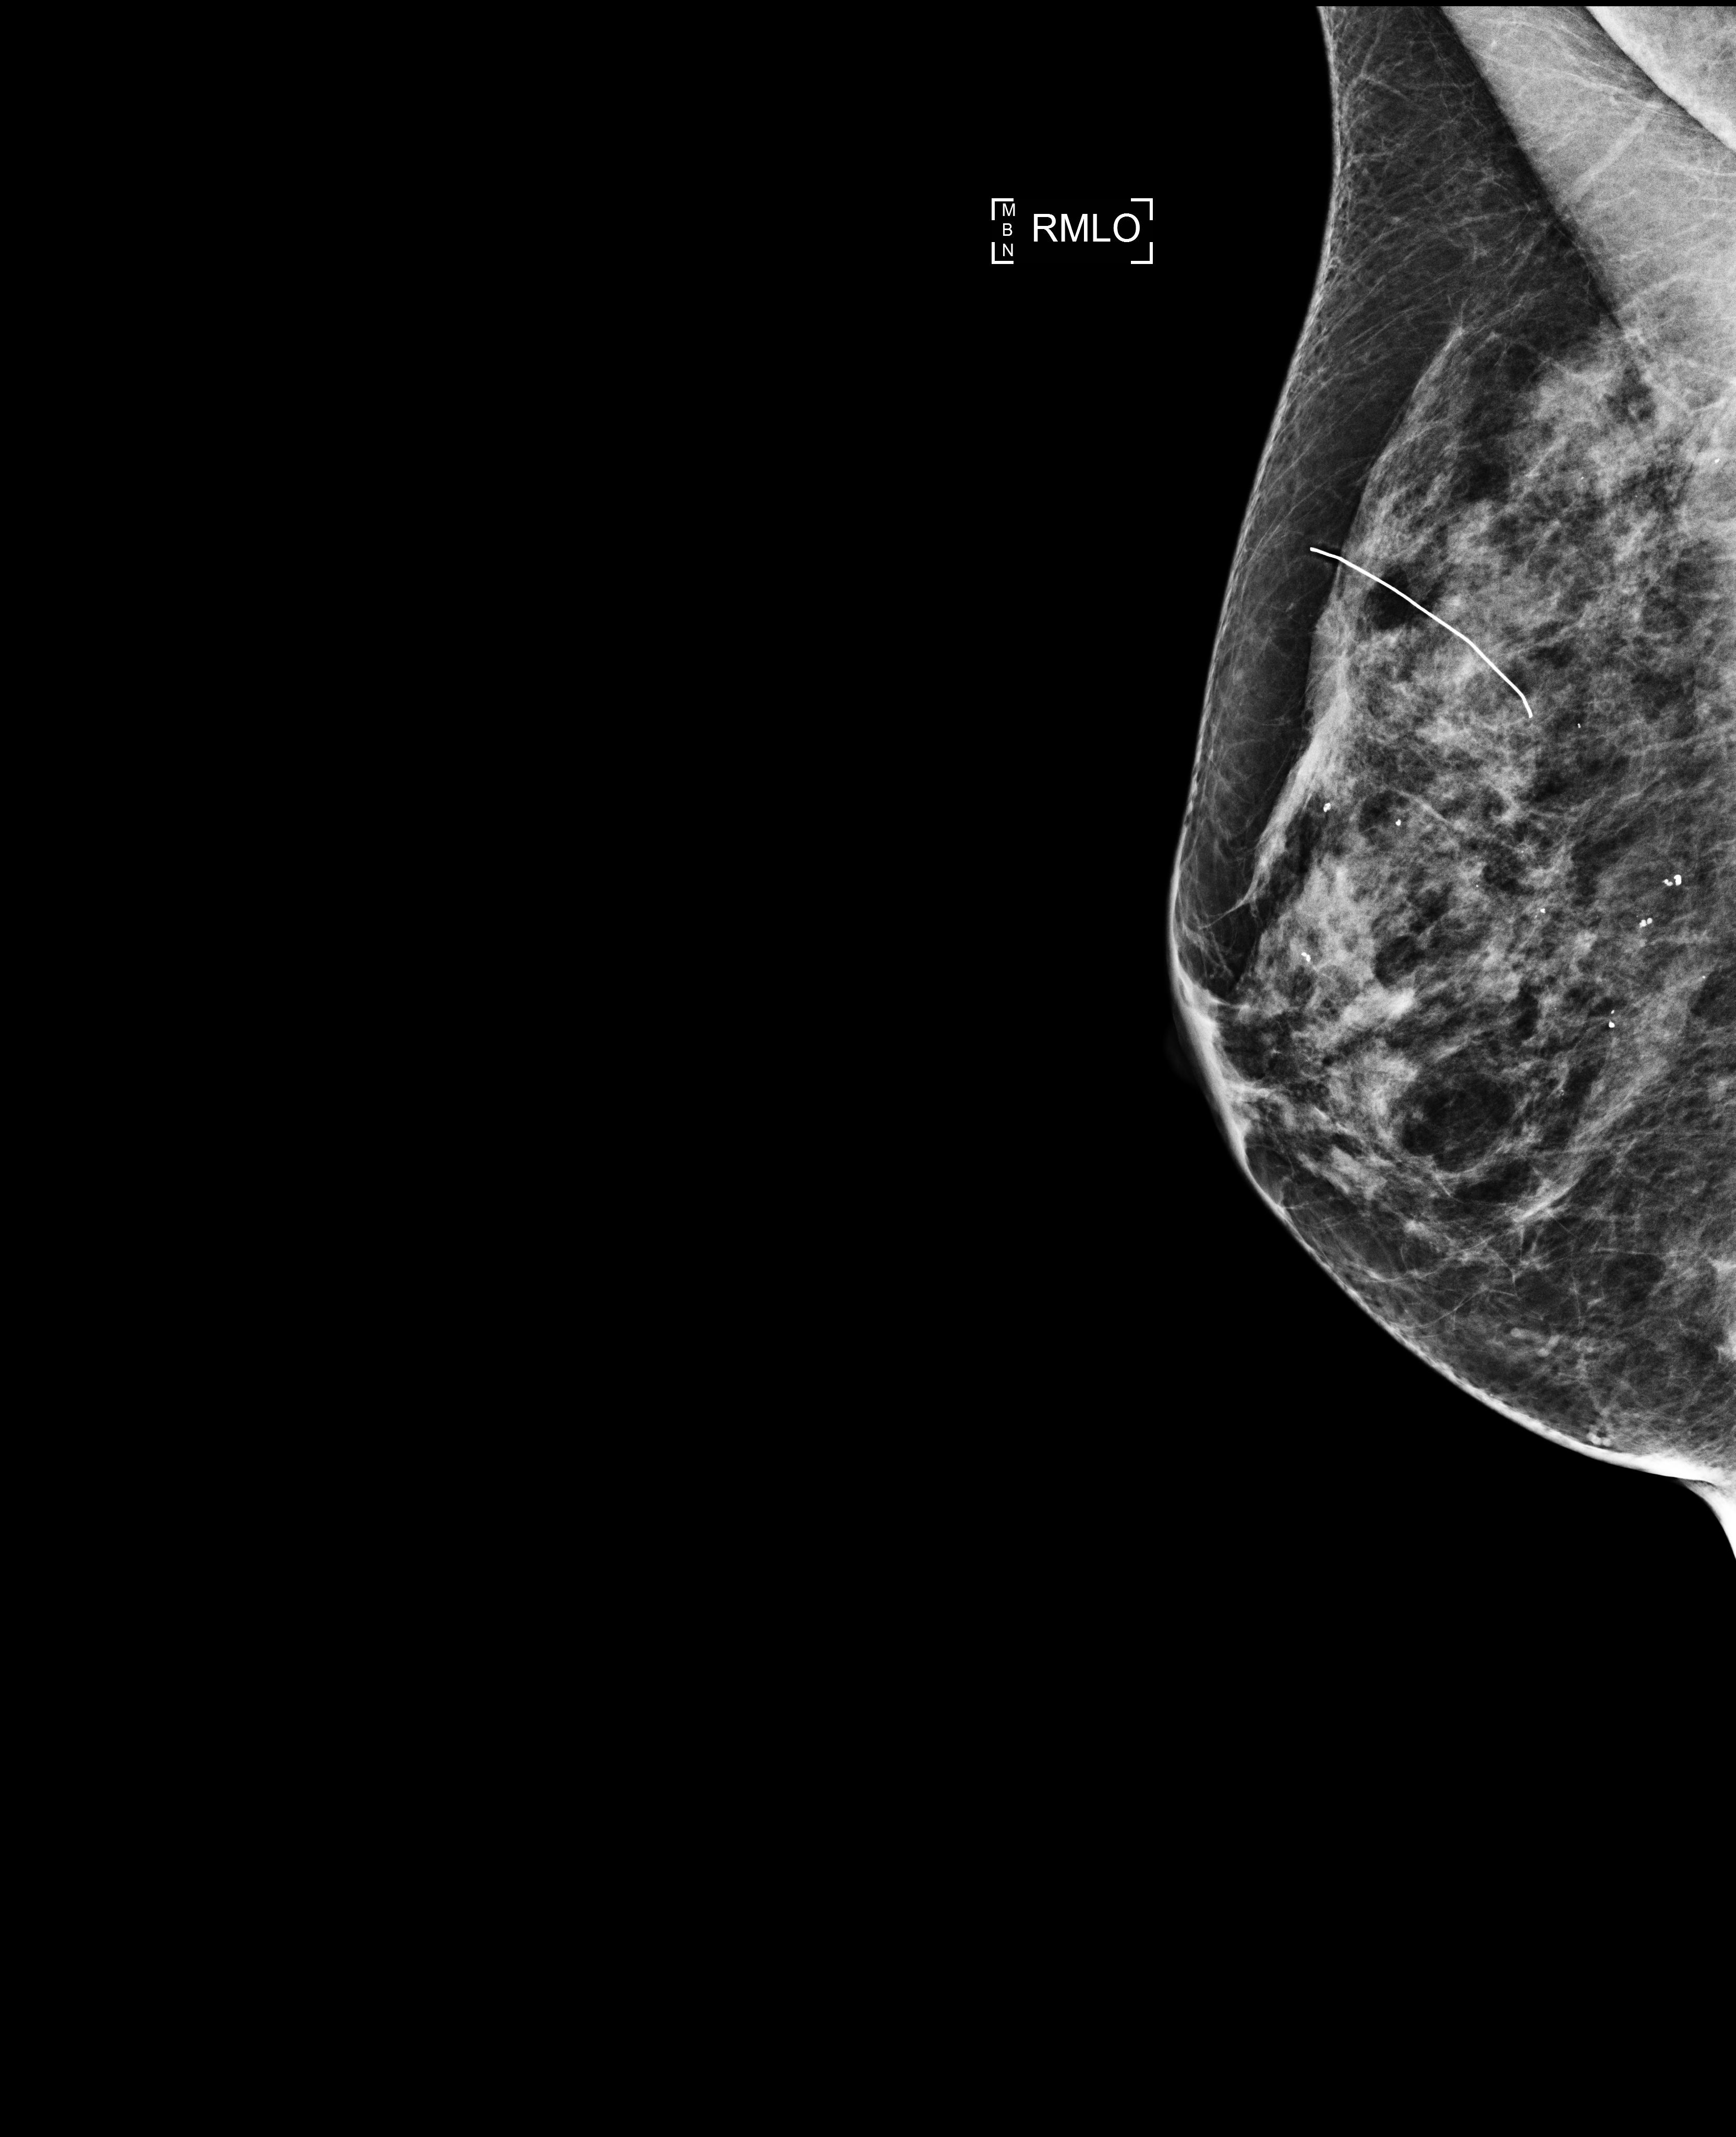
Screening examination; compressed breast thickness 46 mm; system: Selenia Dimensions. Patient aged 75 years (female).
Image type: full-field digital mammogram. Breast: right. Projection: mediolateral oblique (MLO) view.